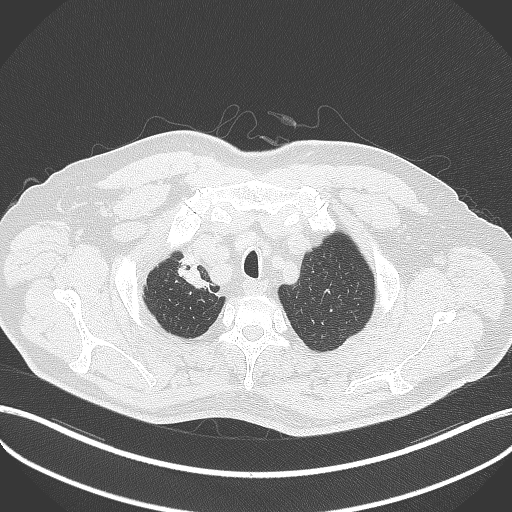
Chest CT, one axial slice; reconstruction kernel B70f; 120 kVp; lung window (W 1500 / L -600 HU); 512 × 512 image matrix, field of view 400 × 400 mm. Patient: male, 60 years. From the clinical record (not read from this slice): clinical TNM (as recorded): T1b N1 M0.
Annotated regions visible in this slice (rectangle marked by the reading radiologist):
- lung tumour (recorded histology: squamous cell carcinoma): bounding box (x1, y1, x2, y2) in pixels: (174, 249, 210, 294)